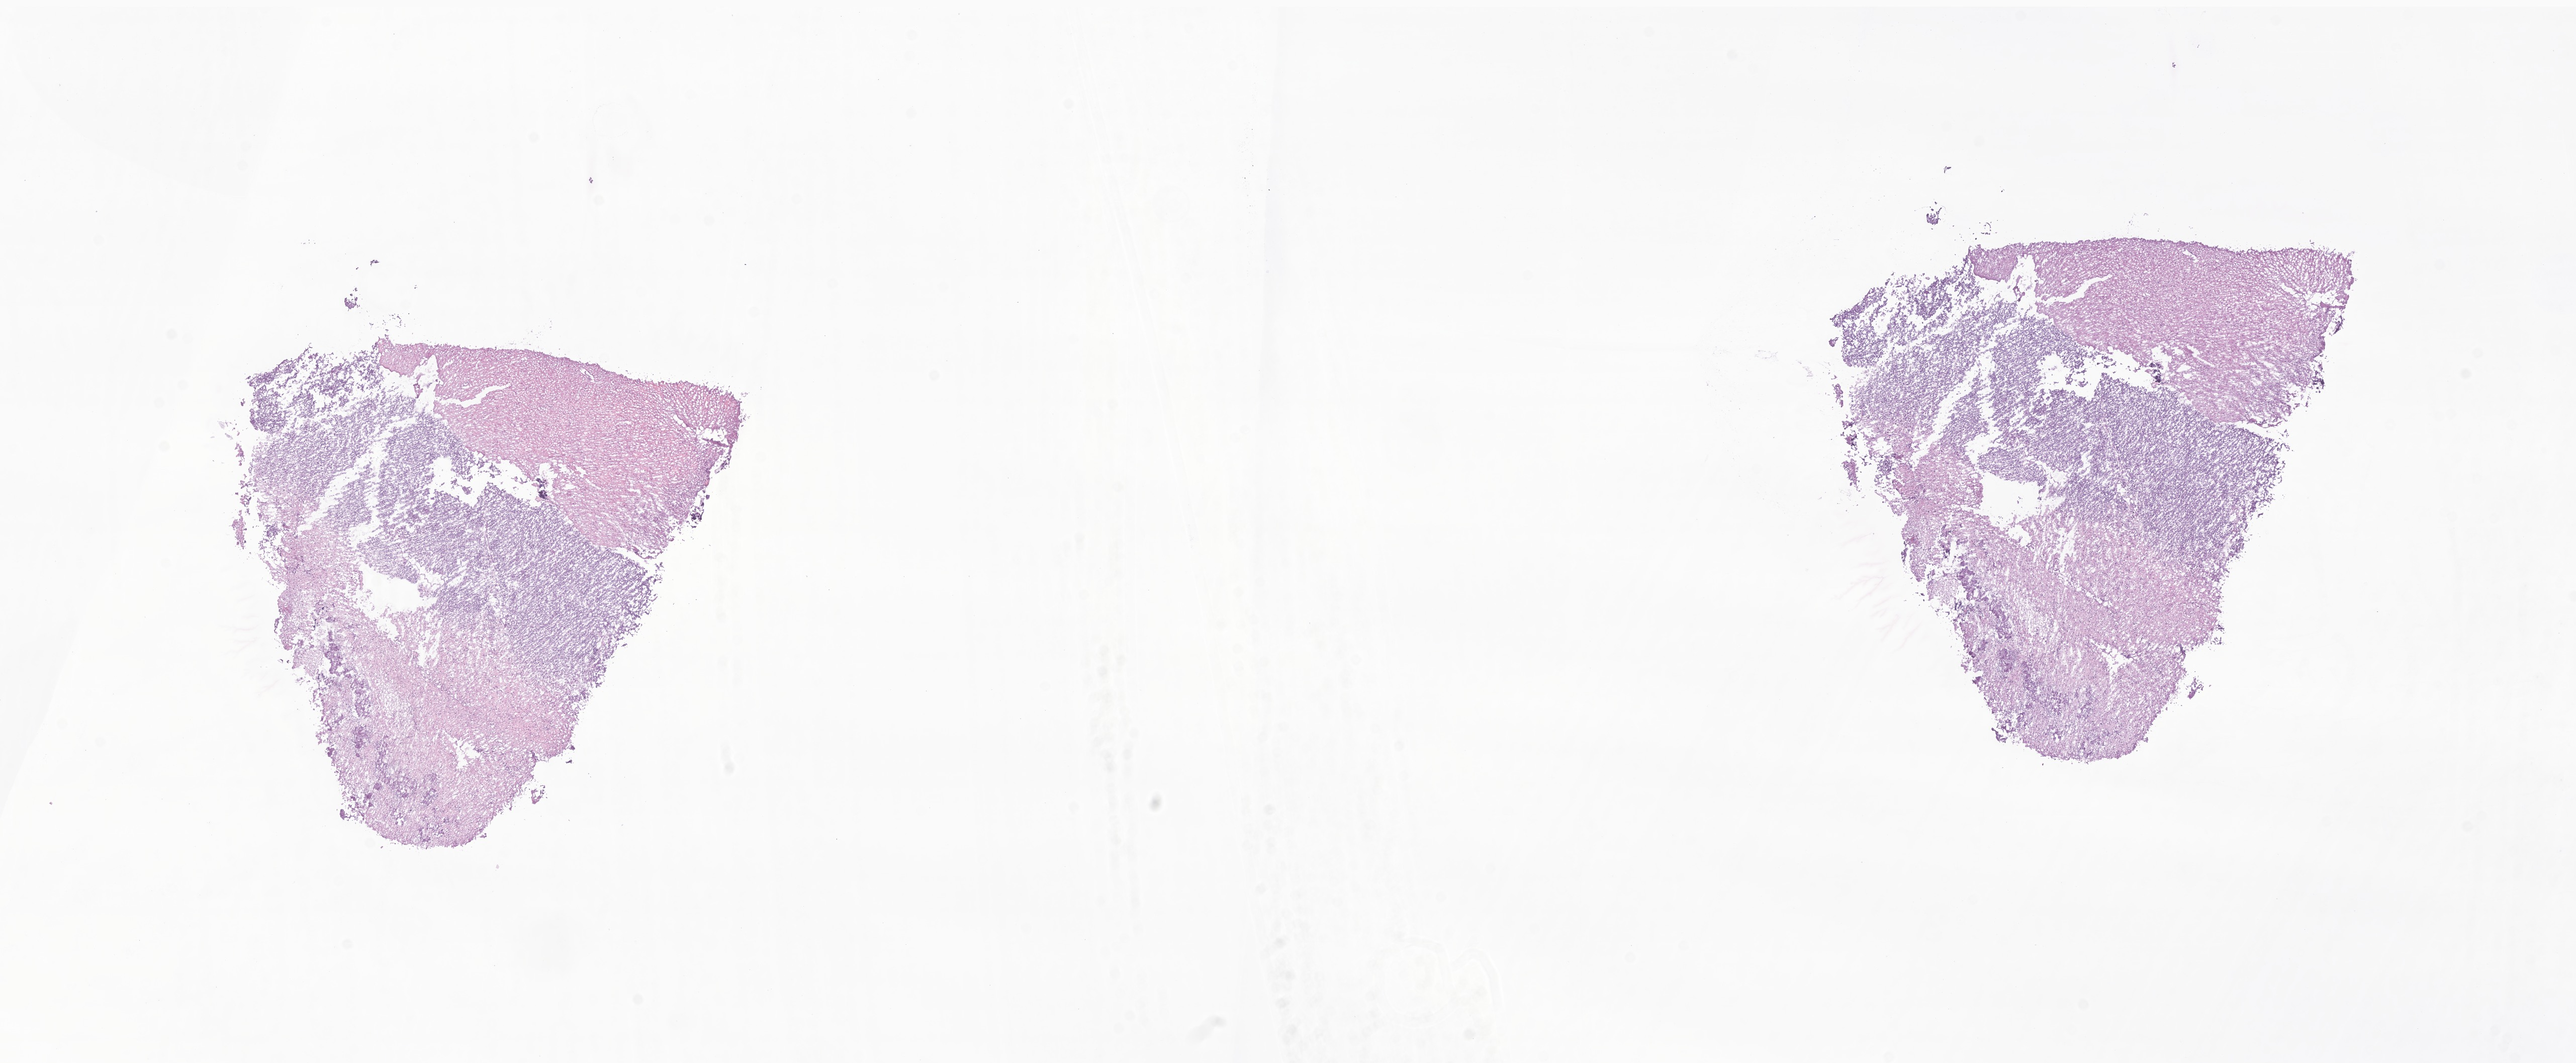
Digitized hematoxylin and eosin (H&E)-stained section of tumor tissue from the brain, shown as a low-resolution overview of the whole scanned area (about 21.6 x 8.9 mm). Cryosection (OCT / tissue freezing medium). Patient: male, age 138 months (11 years 6 months).
* recorded diagnosis: Glioma, malignant